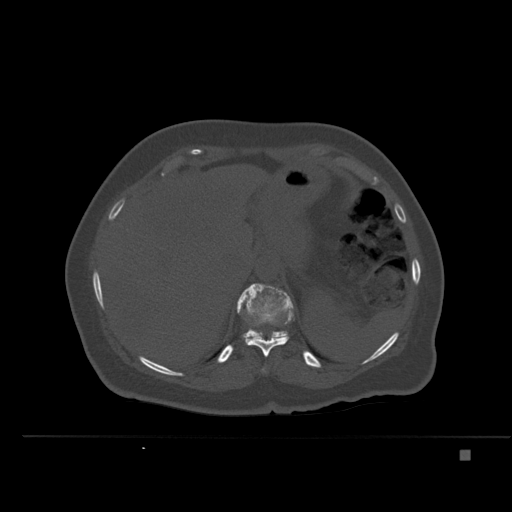
CT including the spine, one axial slice. Slice 265 of 477 in the series (ordered by position). Bone window (W 1800 / L 400 HU). 1.5 mm slice thickness. 512 × 512 image matrix, field of view 422 × 422 mm. Patient: female, 74 years. From the clinical record (not read from this slice): primary cancer: colon.
Structures marked on this image (semi-automatically segmented with operator editing):
- L1 vertebra: bounding box (x1, y1, x2, y2) in pixels: (249, 320, 275, 324)
- T10 vertebra: (262, 369, 265, 372)
- T11 vertebra: (244, 320, 289, 357)
- T12 vertebra: (237, 283, 294, 338)